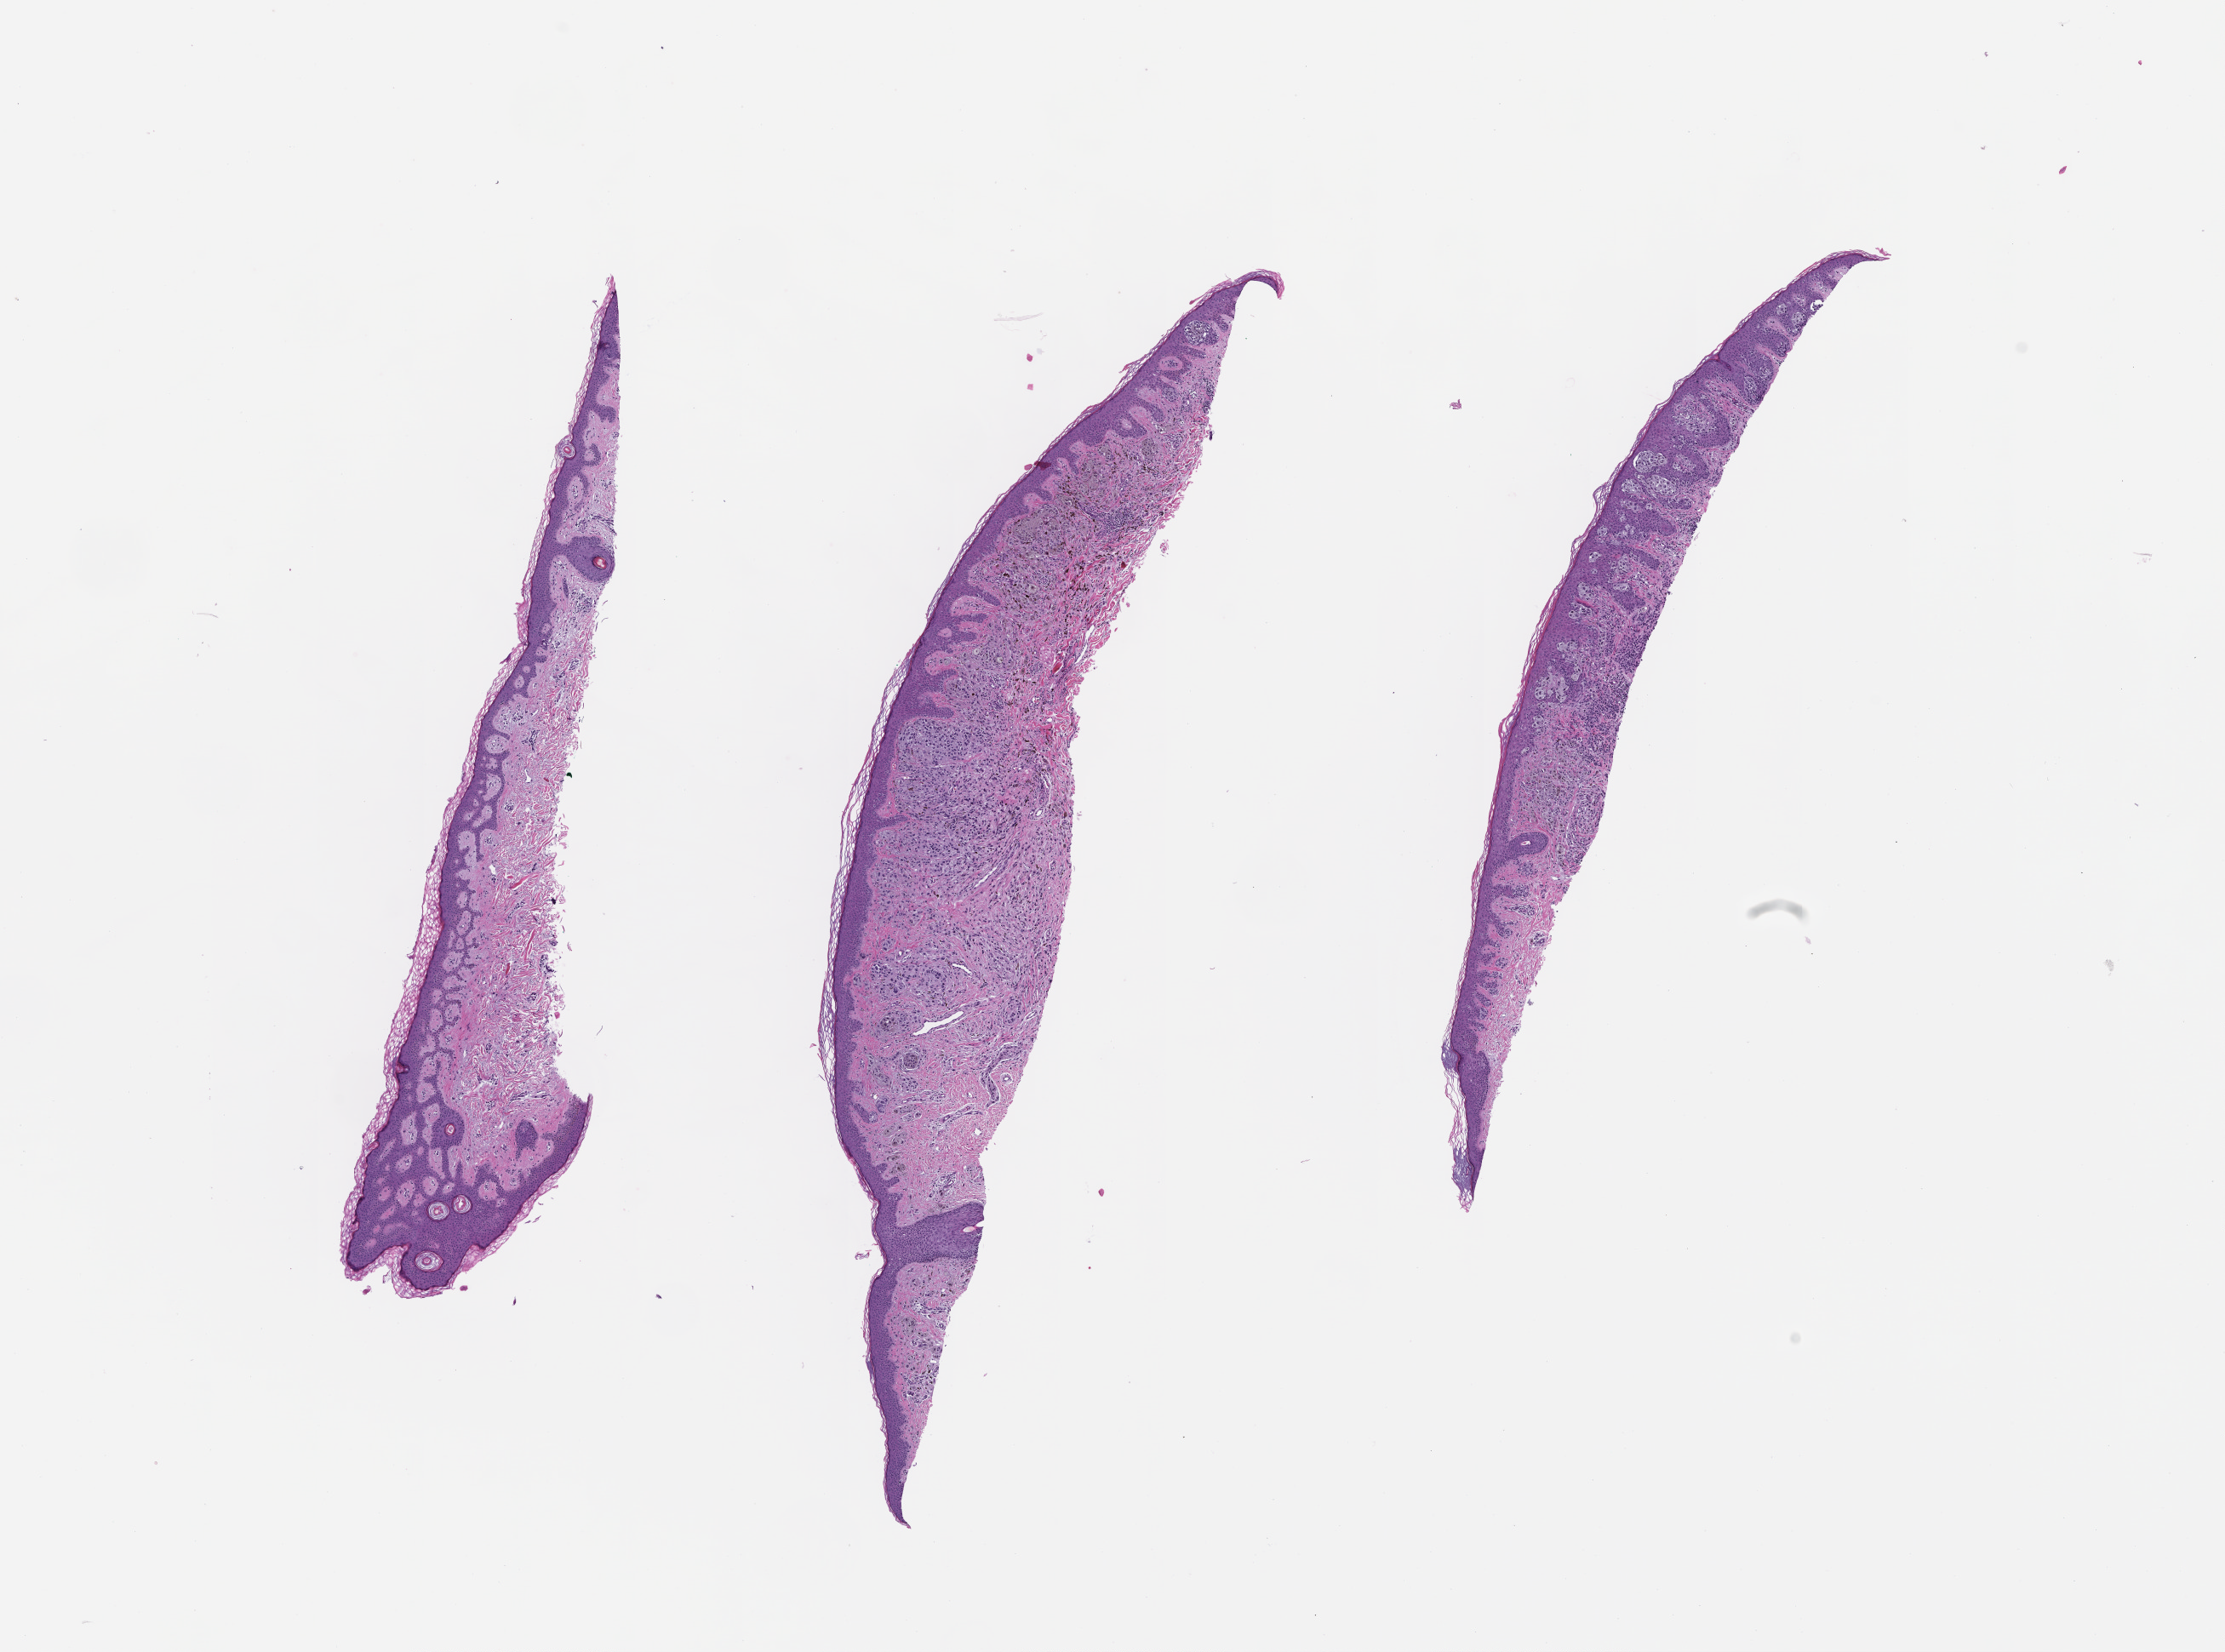
Whole-slide image, H&E stain, a low-resolution overview of the entire scanned area, about 10.6 x 7.8 mm; formalin-fixed paraffin-embedded section; site: skin. Male patient.
* this section: primary tumour tissue
* diagnosis: Melanoma